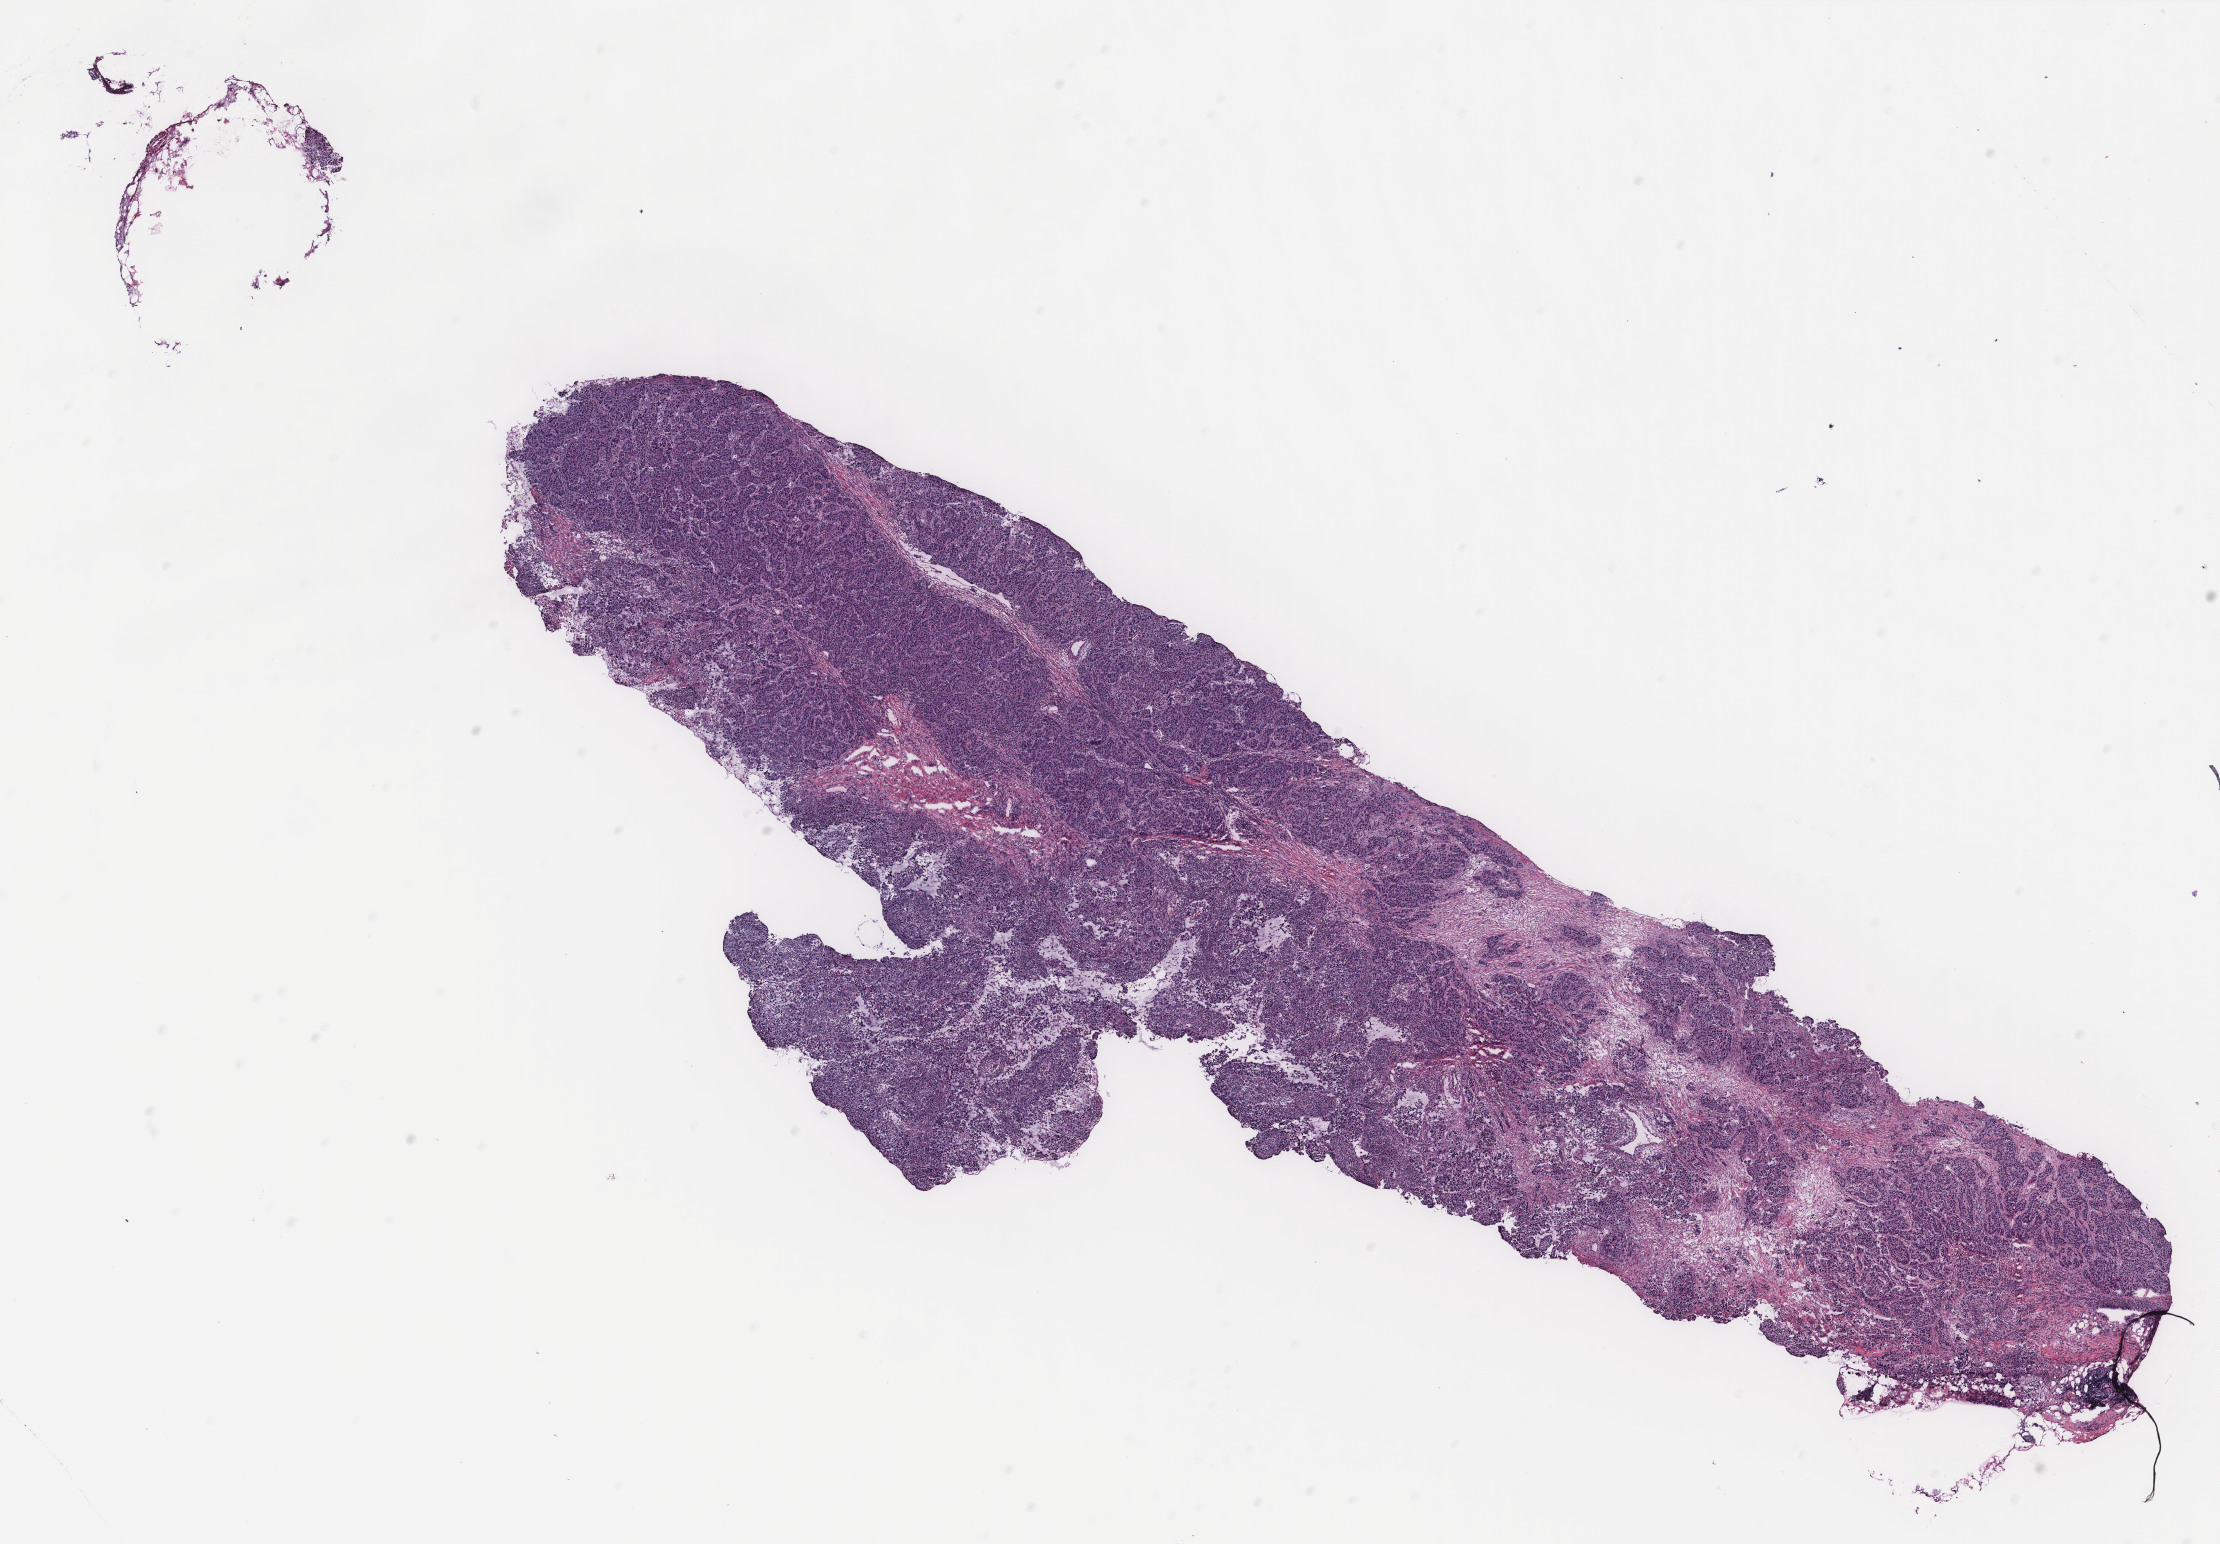
Whole-slide histology image, H&E-stained — shown as a low-resolution overview of the whole scanned area (about 17.8 x 12.4 mm). Breast, tissue type not recorded. 79-year-old female patient.
Patient diagnosis: Infiltrating duct carcinoma, NOS.